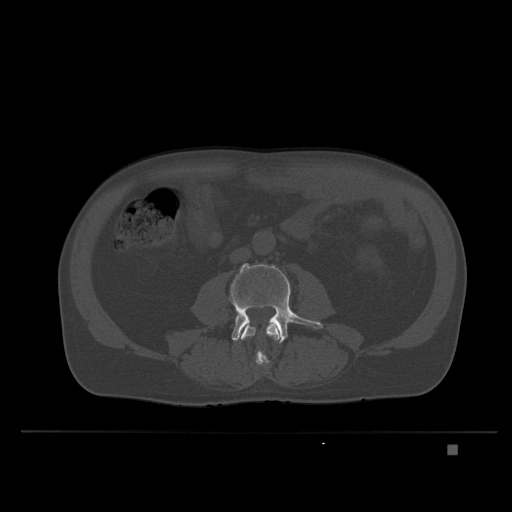
CT including the spine, one axial slice; slice 83 of 435 in the series (ordered by position); bone window (W 1800 / L 400 HU); 512 × 512 image matrix. Male patient, age 73 years. From the clinical record (not read from this slice): primary cancer: skin.
Annotated regions visible in this slice (semi-automatic segmentation, software-assisted and operator-edited):
- L3 vertebra: bounding box <240,320,282,368> (left, top, right, bottom; pixels)
- L4 vertebra: <211,263,323,344>